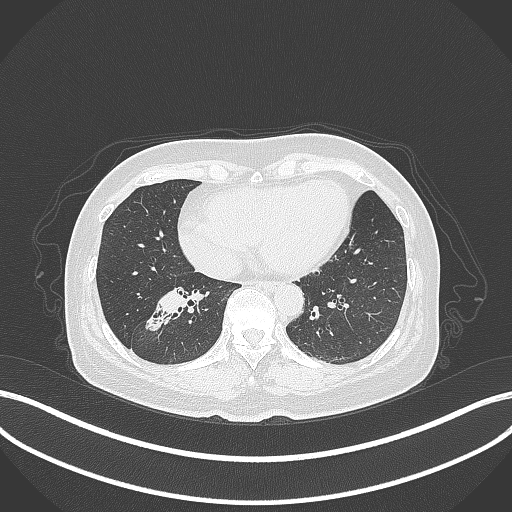
Chest CT, one axial slice. Position 136 of 429 along the scan axis. Reconstruction kernel B70f. 120 kVp. Lung window (W 1500 / L -600 HU). 1 mm slice thickness. 512 × 512 image matrix, field of view 400 × 400 mm. Female patient, age 67 years. From the clinical record (not read from this slice): clinical TNM (as recorded): T1c N1 M0.
Structures marked on this image (bounding box drawn by a radiologist):
- lung tumour (recorded histology: adenocarcinoma): bounding box <141,287,194,331> (left, top, right, bottom; pixels)